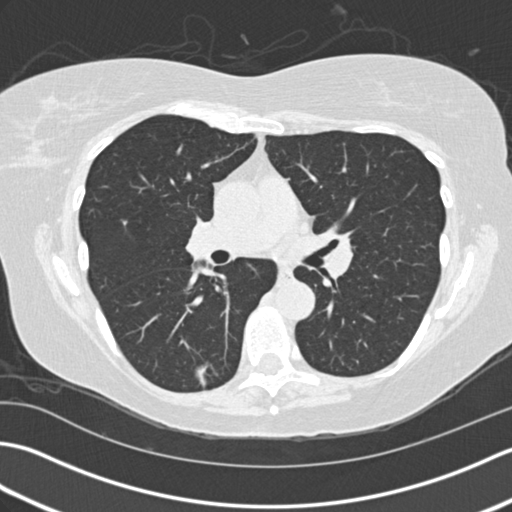
Low-dose screening chest CT, one axial slice. Slice 87 of 159 in the series (ordered by position). Reconstruction kernel B30f. 120 kVp. Lung window (W 1500 / L -600 HU). 2 mm slice thickness. 512 × 512 image matrix, field of view 350 × 350 mm.
Outlined on this slice (outlined manually by an expert reader):
- lesion 1 (tumor, lower lobe of right lung): box from (x=196, y=365) to (x=208, y=387) px